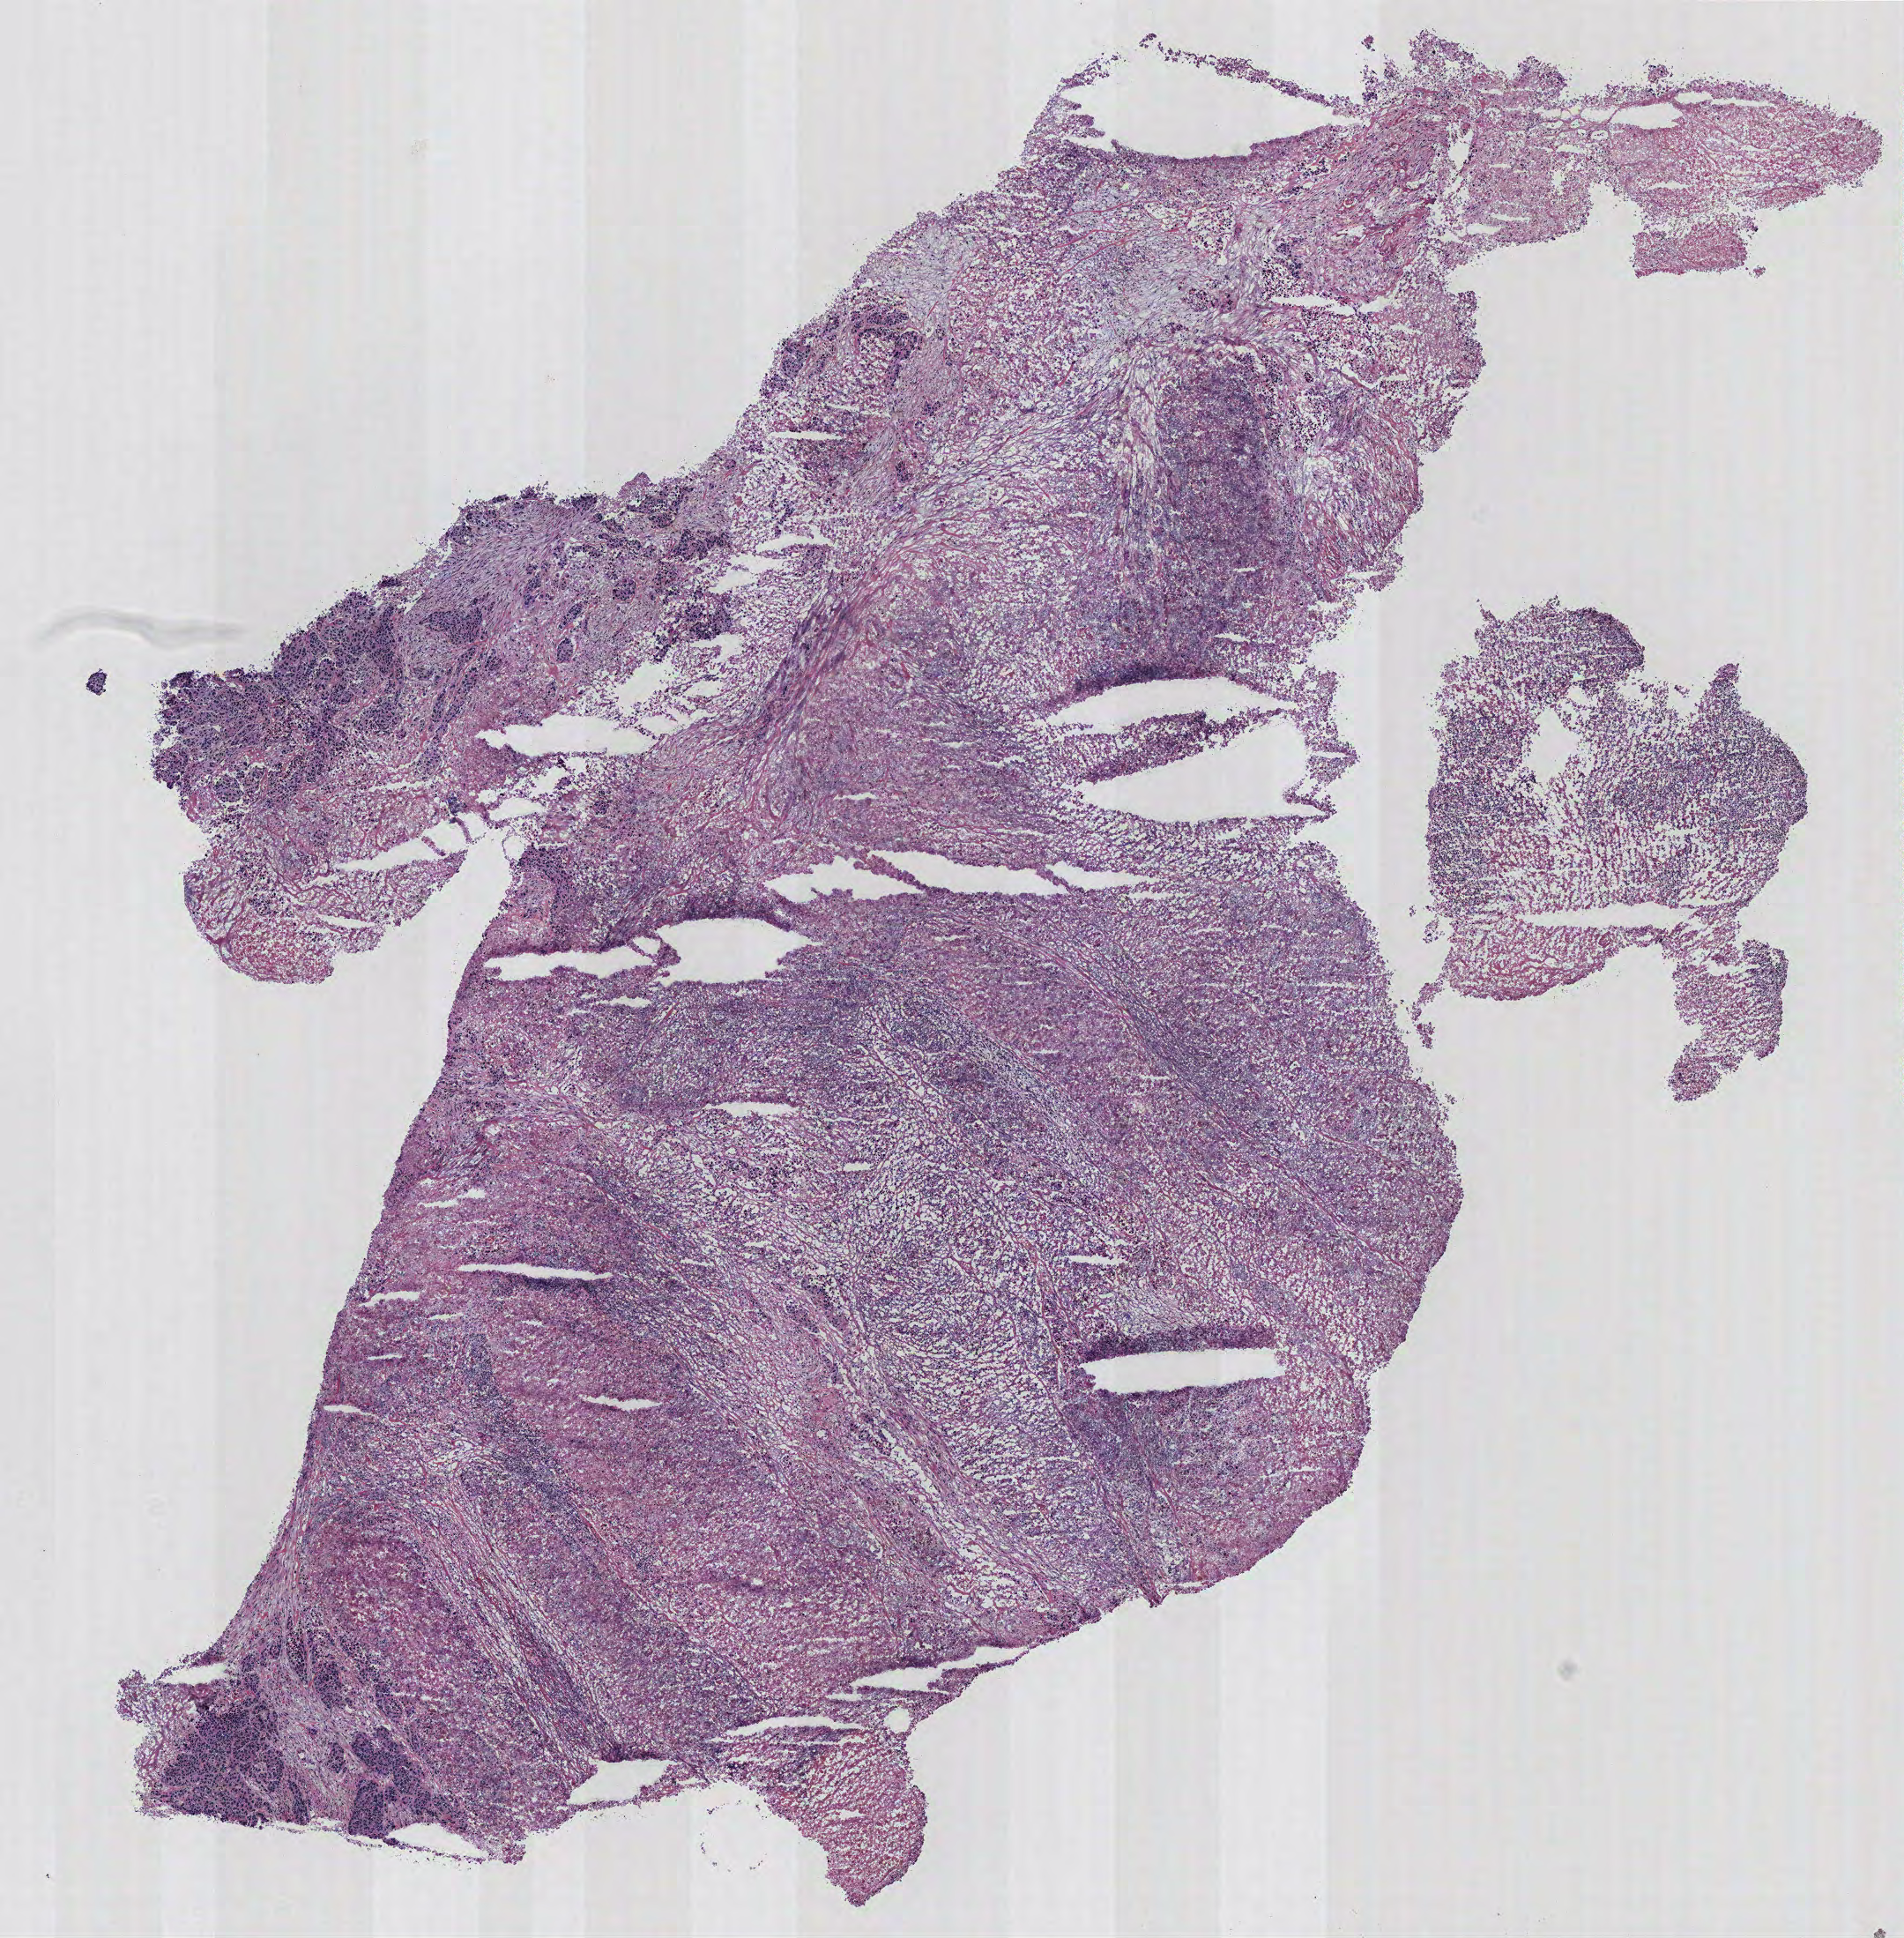
Hematoxylin and eosin (H&E) stained whole-slide image, low-resolution overview of the scanned area, about 8.6 x 8.8 mm. Tumour tissue sample, colon. Female, 70 y/o.
AJCC pathologic stage: IIB. Primary tumour site (as recorded): colon. Histologic diagnosis: Adenocarcinoma, NOS.